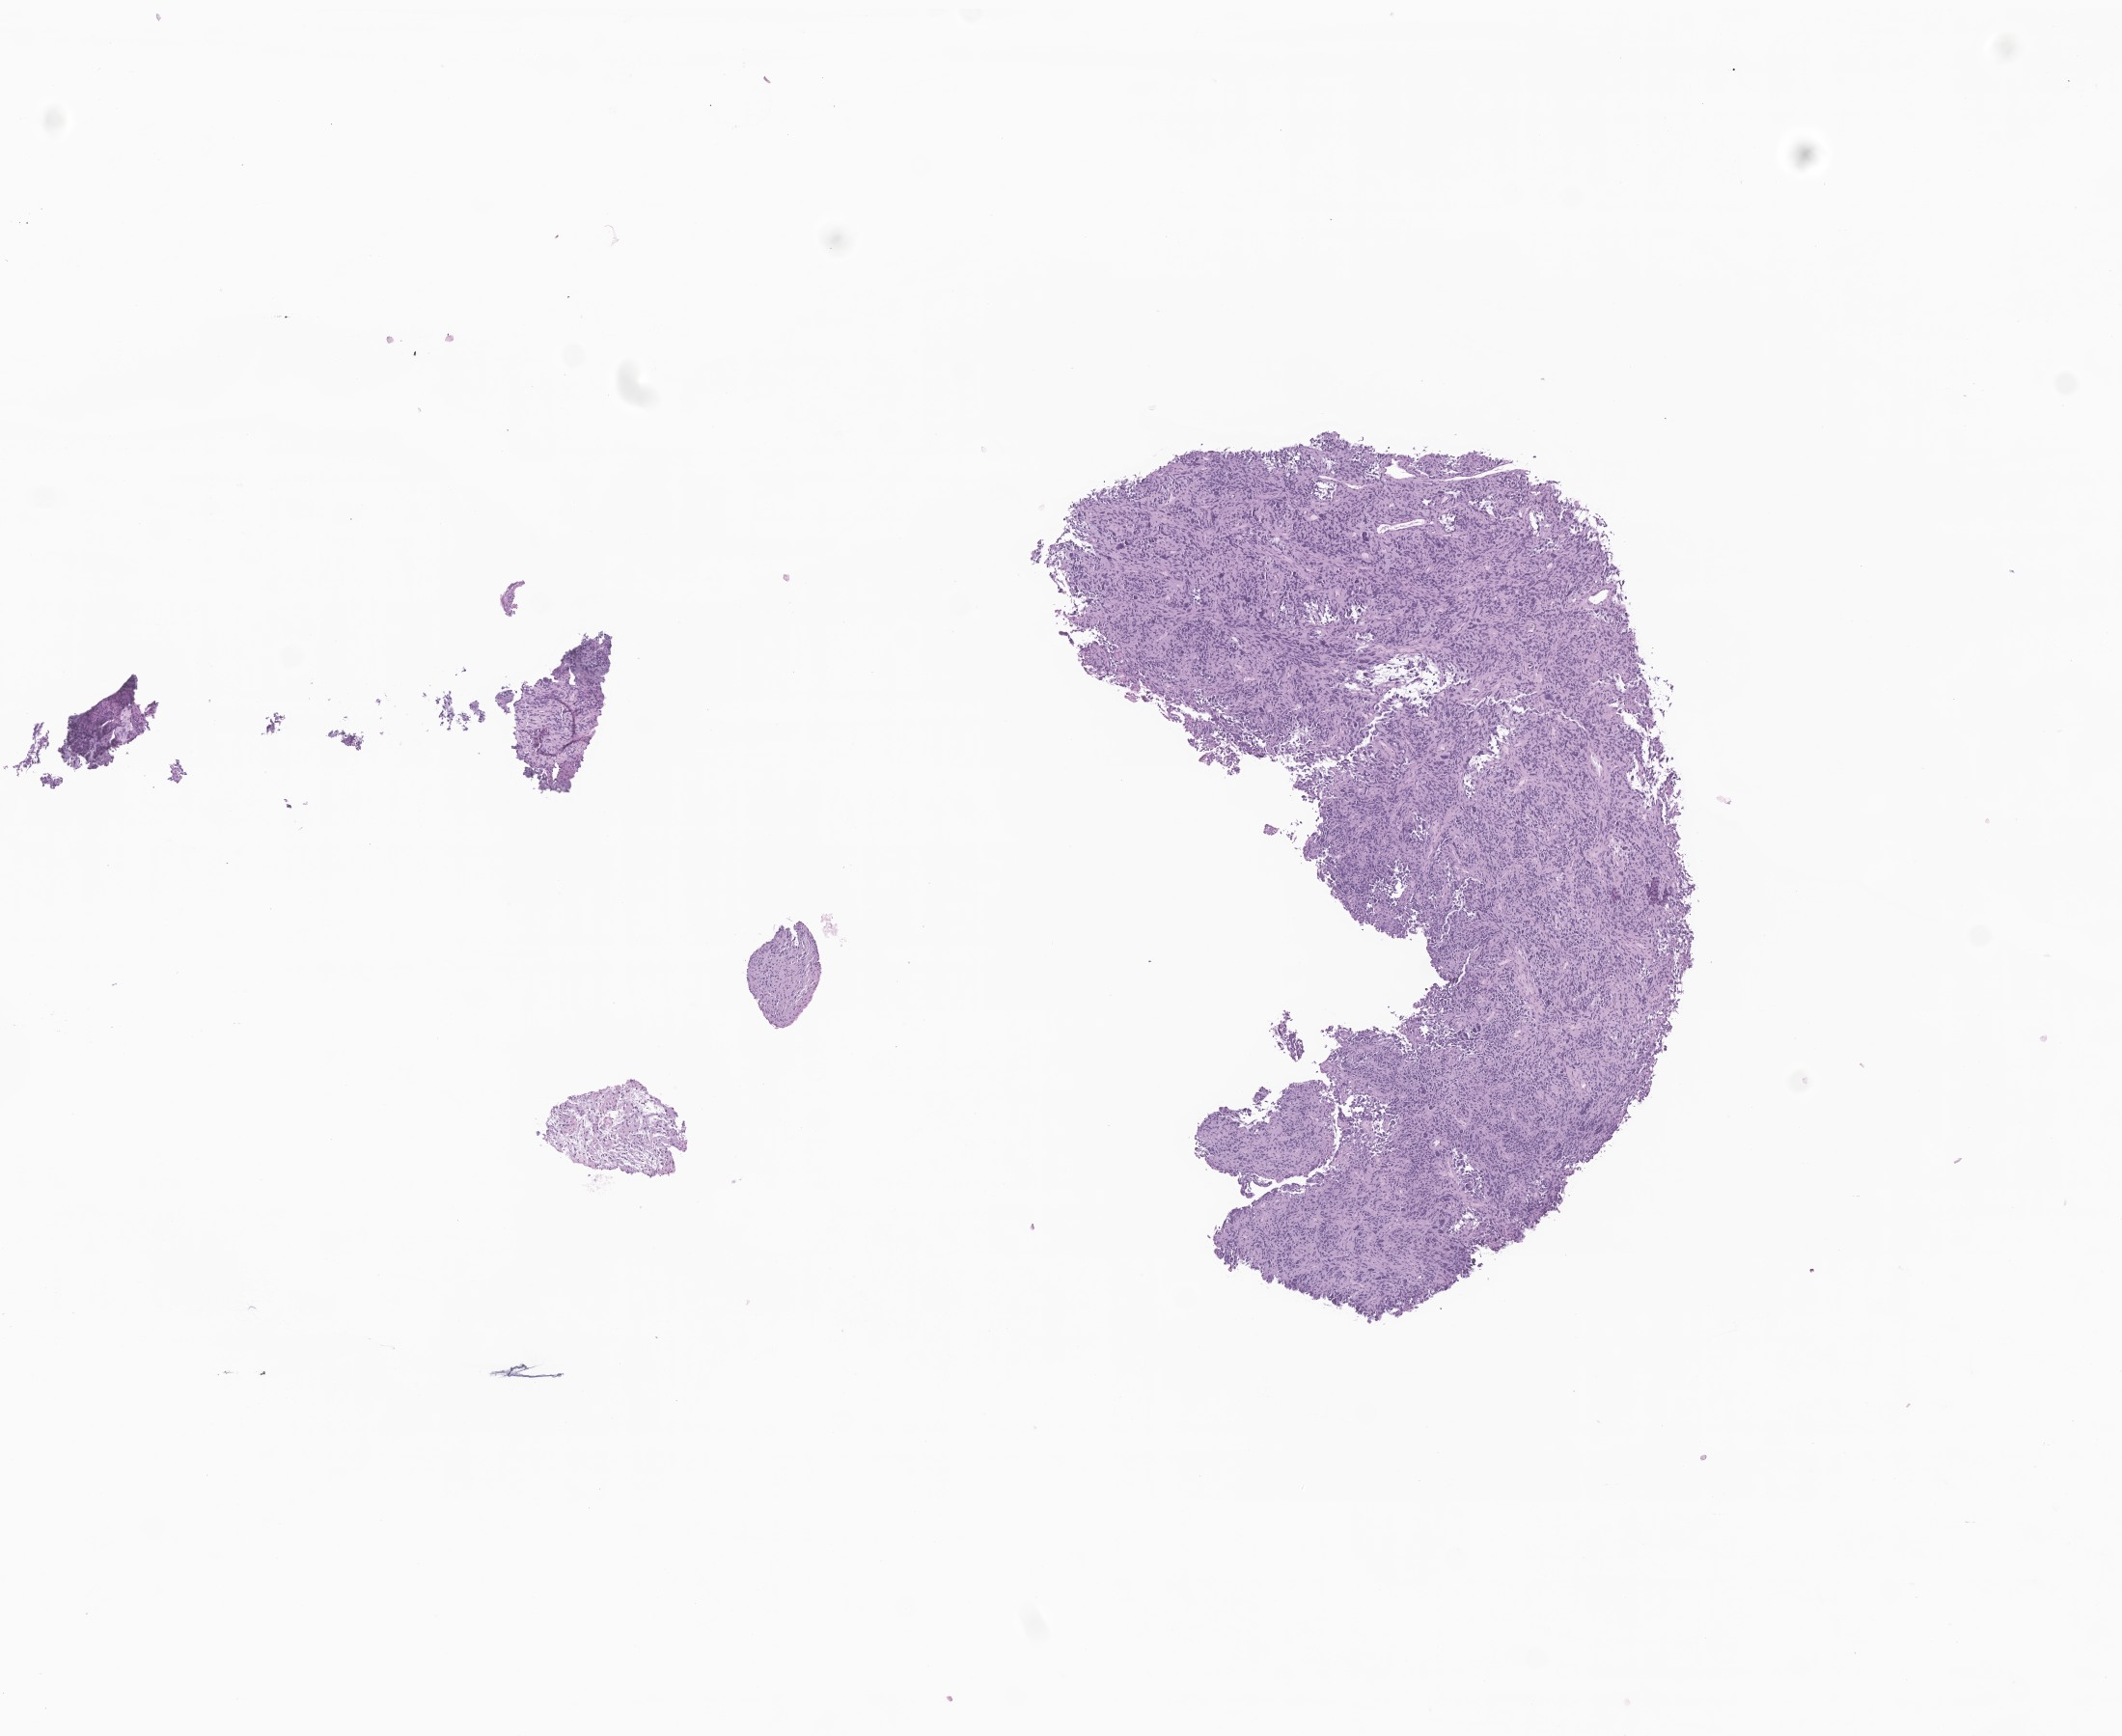
Digitized H&E-stained section of tumor tissue from the brain, a low-resolution overview of the entire scanned area, about 9.3 x 7.6 mm; formalin-fixed paraffin-embedded section. Patient male; age 182 months (15 years 2 months).
* recorded diagnosis: Glioma, malignant